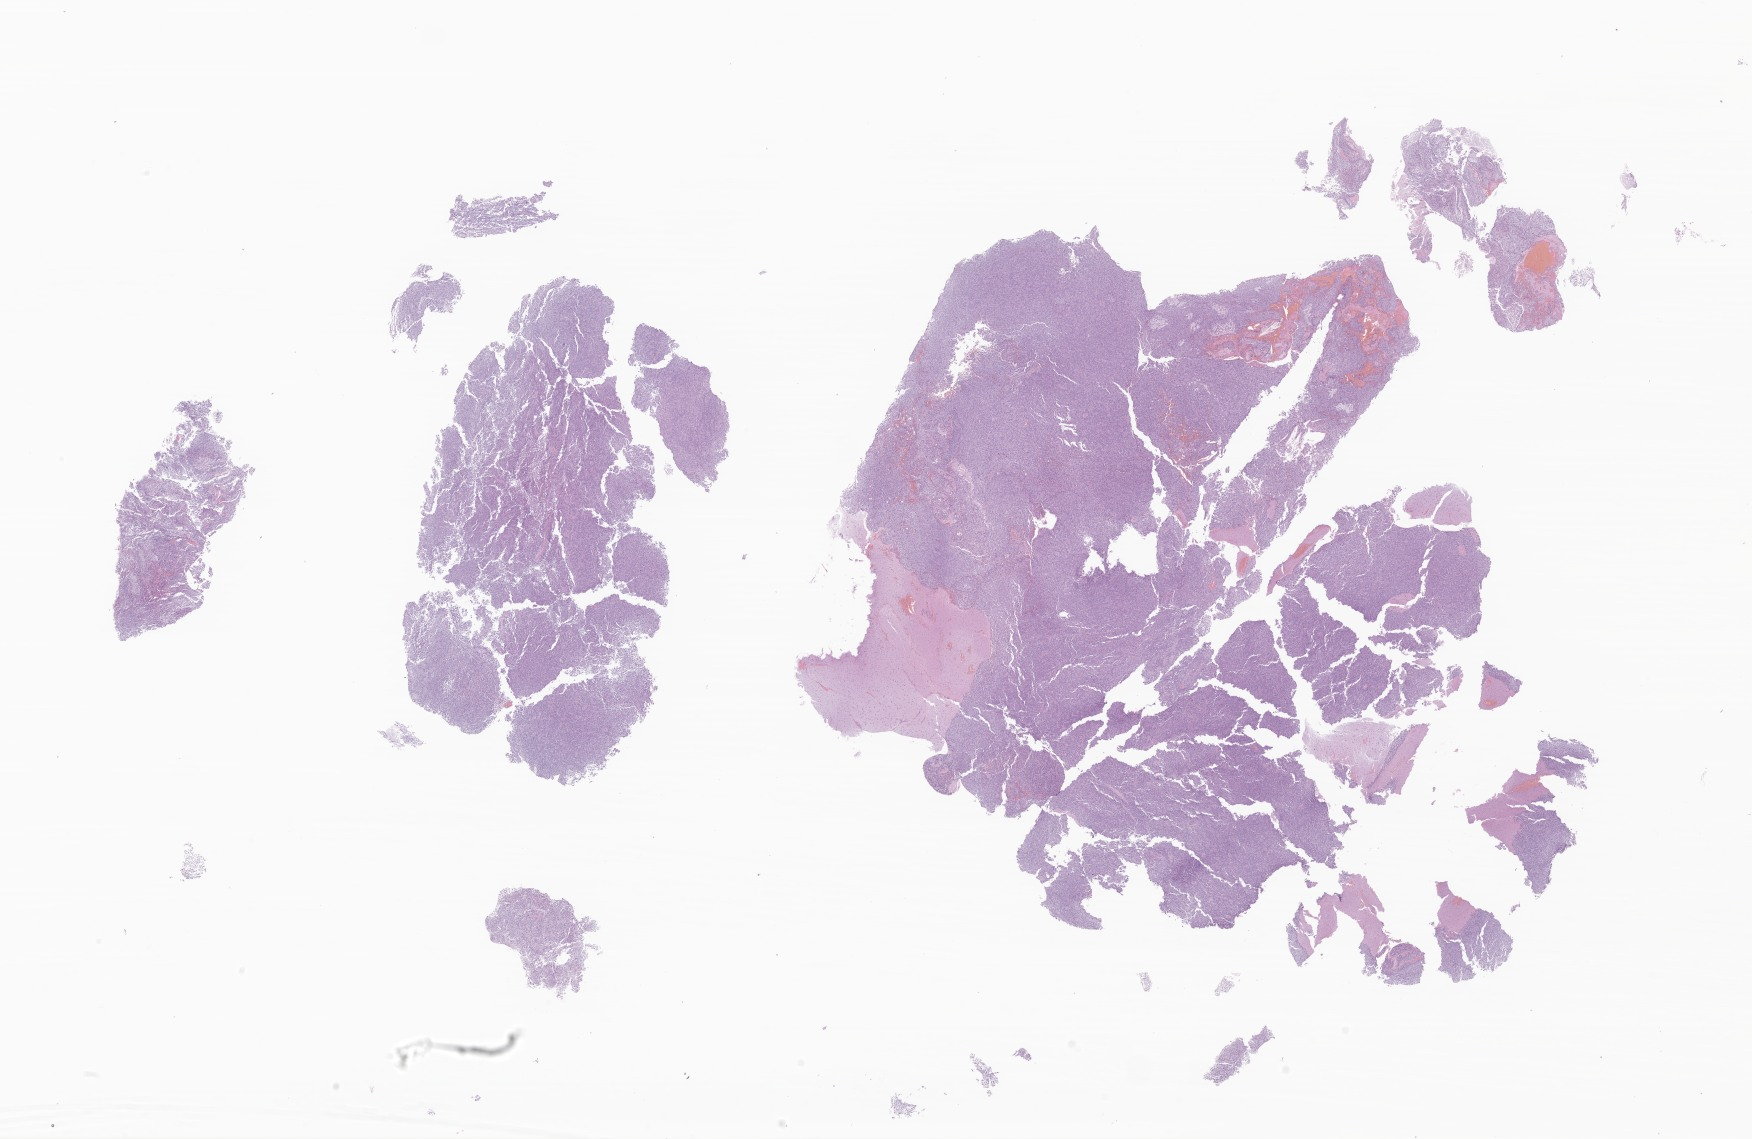
Digitized H&E-stained section of tumor tissue from the brain, shown as a low-resolution overview of the whole scanned area (about 29.6 x 19.2 mm), FFPE section. Patient female; age 136 months (11 years 4 months).
• diagnosis: Astroblastoma